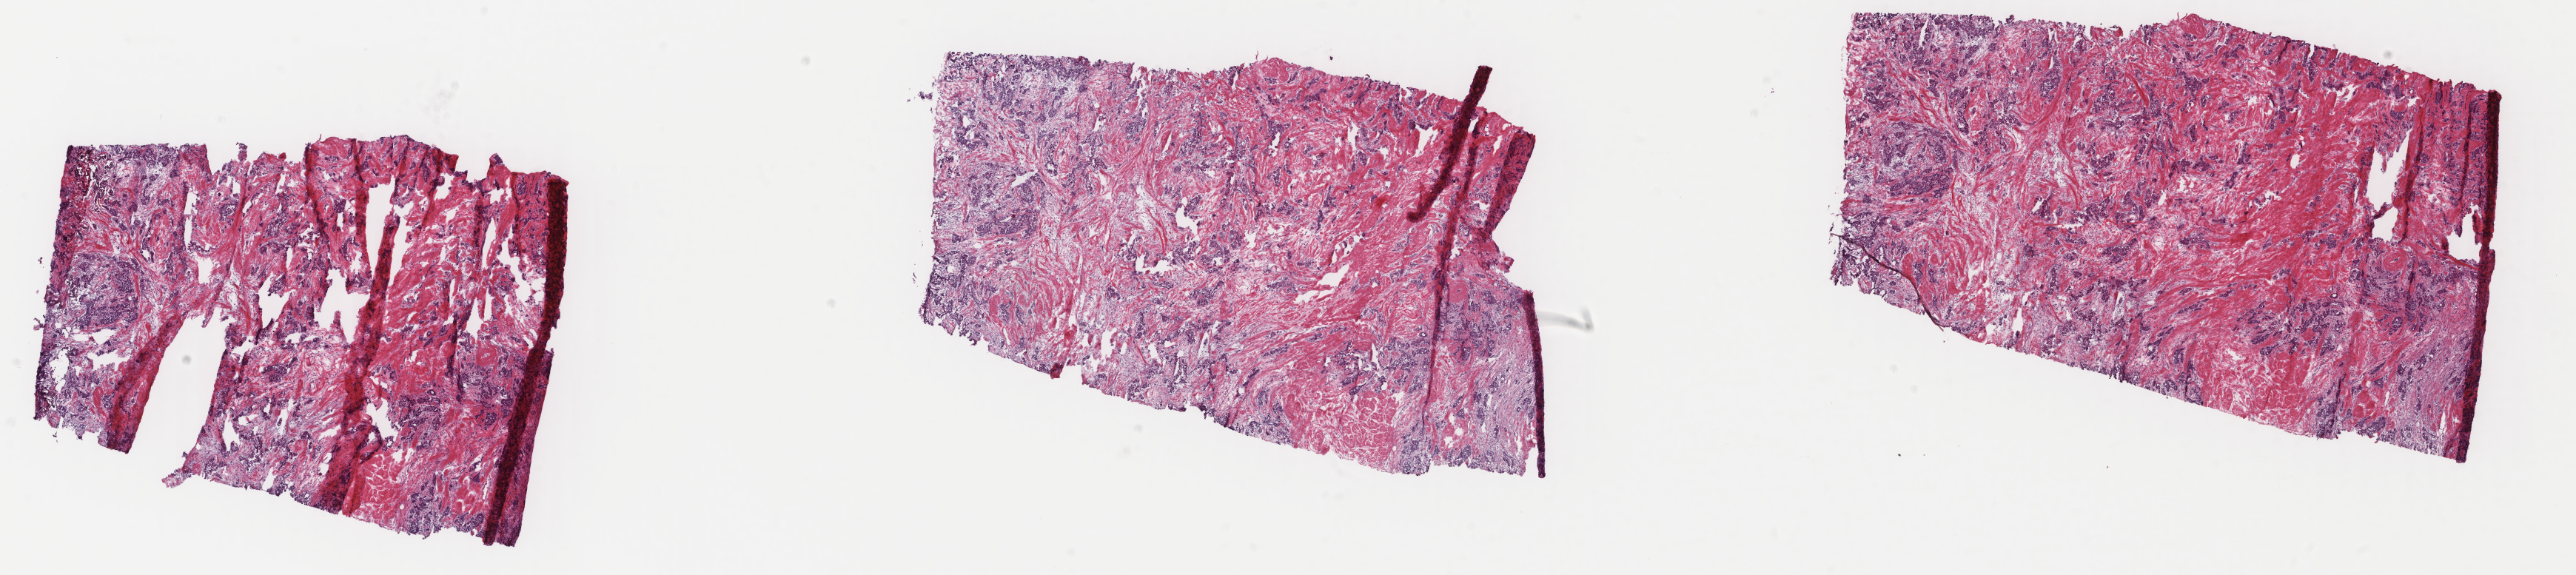
Digitized H&E tissue section (whole slide), shown as a low-resolution overview of the whole scanned area (about 27.6 x 6.2 mm, acquisition: 40x scan), frozen section, sample: primary tumour, breast. Patient: female, age at initial diagnosis 70 years. Pathologist review of this section (percent, as recorded): tumour cells 15%, tumour nuclei 15%, normal cells 0%, stromal cells 84%, necrosis 1%. Inflammatory infiltration, as recorded: lymphocyte infiltration 0%, monocyte infiltration 0%, neutrophil infiltration 0%.
Histologic diagnosis: Infiltrating duct carcinoma, NOS. Laterality: right. Lymph nodes positive (case pathology): 5 of 17 examined. TNM: T2 N2a MX. AJCC pathologic stage: IIIA (7th edition).